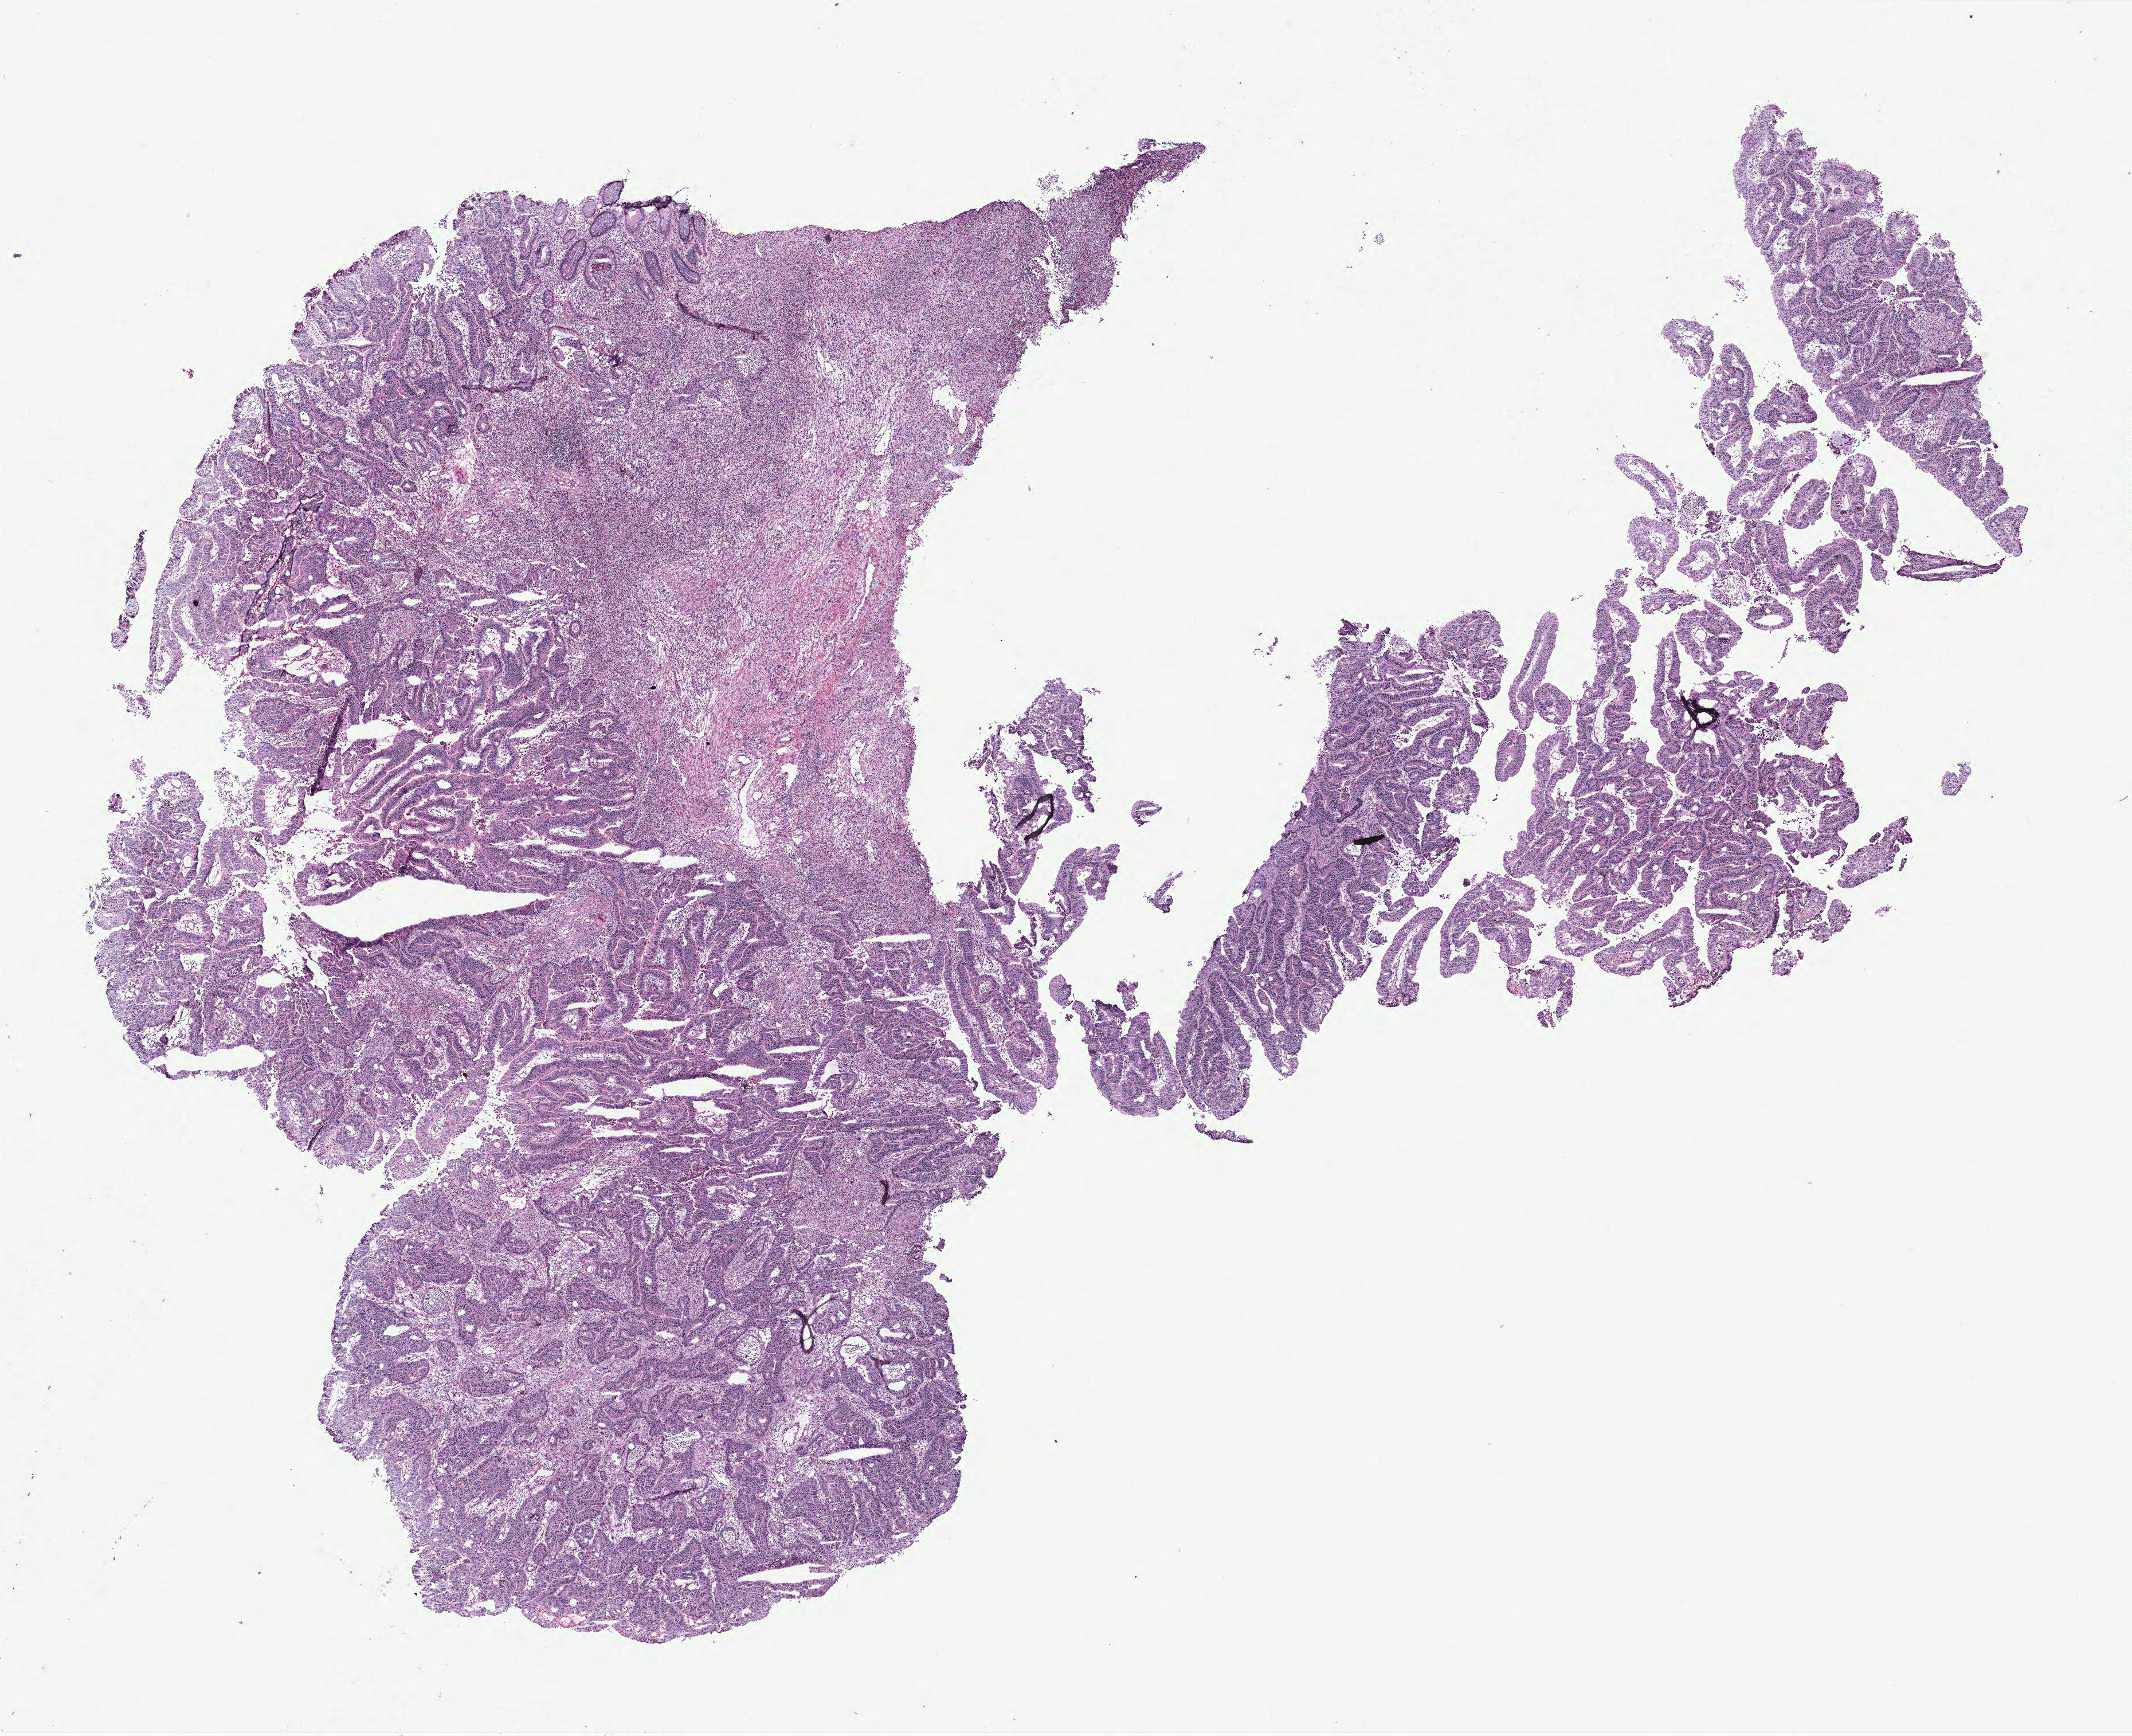
Hematoxylin and eosin (H&E) stained whole-slide image, a low-resolution overview of the entire scanned area, about 14.9 x 12.1 mm (from a 40x scan). Colon, tumour tissue. 52-year-old female patient.
AJCC pathologic stage: IIIA. Diagnosis: Adenocarcinoma, NOS. Primary tumour site (as recorded): colon.